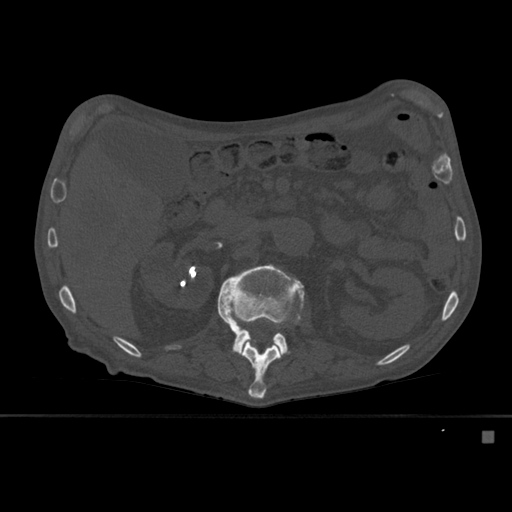
CT including the spine, one axial slice; position 246 of 527 along the scan axis; bone window (W 1800 / L 400 HU); 512 × 512 image matrix, field of view 373 × 373 mm. Patient: male, 78 years. From the clinical record (not read from this slice): primary cancer: prostate.
Structures marked on this image (semi-automatically segmented with operator editing):
- L1 vertebra: bounding box [x1, y1, x2, y2] px = [240, 320, 283, 399]
- L2 vertebra: [217, 264, 306, 357]